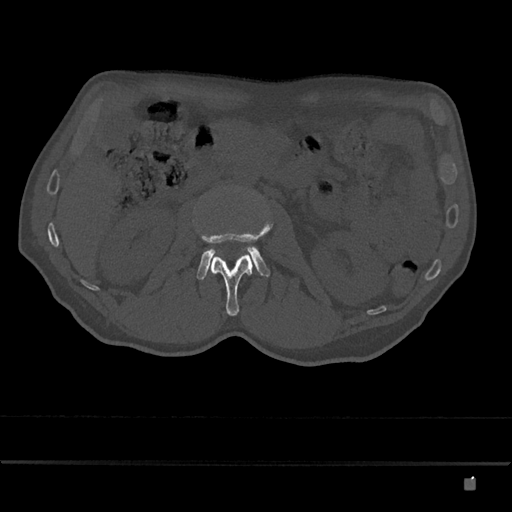
CT including the spine, one axial slice. Slice 452 of 797 in the series (ordered by position). Reconstruction kernel Br40s/3. Bone window (W 1800 / L 400 HU). 512 × 512 image matrix, field of view 390 × 390 mm. Male patient, age 72 years. Case-level facts recorded for this patient, not image findings: primary cancer: prostate.
Outlined on this slice (semi-automatic segmentation, software-assisted and operator-edited):
- L2 vertebra: bounding box [x1, y1, x2, y2] px = [198, 221, 273, 316]
- L3 vertebra: [194, 207, 270, 280]